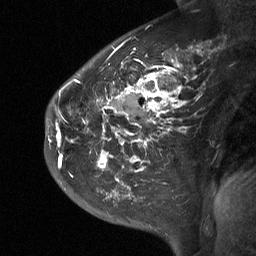
Breast MRI (dynamic contrast-enhanced), one sagittal slice. Position 41 of 64 along the scan axis. Dynamic contrast-enhanced study with each time point stored as its own series, time point 2 of 3 at this slice position (early post-contrast, ordered by acquisition time). 1.5 T. TE 4.8 ms, TR 27 ms. 2 mm slice thickness. 256 × 256 image matrix, field of view 200 × 200 mm. Female patient, age 42 years. From the clinical record (not read from this slice): setting: breast cancer imaged before/during neoadjuvant chemotherapy; receptor status: triple-negative.
Structures marked on this image (semi-automatically segmented with operator editing):
- analysis volume of interest (the breast-tissue region the enhancement analysis was run in; not a lesion): bounding box <45,29,203,190> (left, top, right, bottom; pixels)
- tumour enhancement mask (voxels above the 90 % enhancement threshold inside the analysis volume of interest): <48,49,184,172>